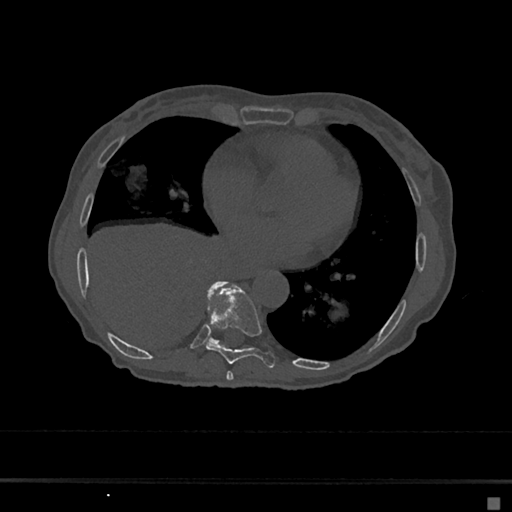
CT including the spine, one axial slice. Slice 314 of 797 in the series (ordered by position). Reconstruction kernel Br40s/3. Bone window (W 1800 / L 400 HU). 0.5 mm slice thickness. 512 × 512 image matrix, field of view 360 × 360 mm. Patient: female, 68 years. Case-level facts recorded for this patient, not image findings: primary cancer: renal.
Structures marked on this image (semi-automatic segmentation, software-assisted and operator-edited):
- T7 vertebra: box from (x=226, y=371) to (x=234, y=381) px
- T8 vertebra: (x=206, y=288)–(x=276, y=368)
- T9 vertebra: (x=209, y=281)–(x=226, y=344)